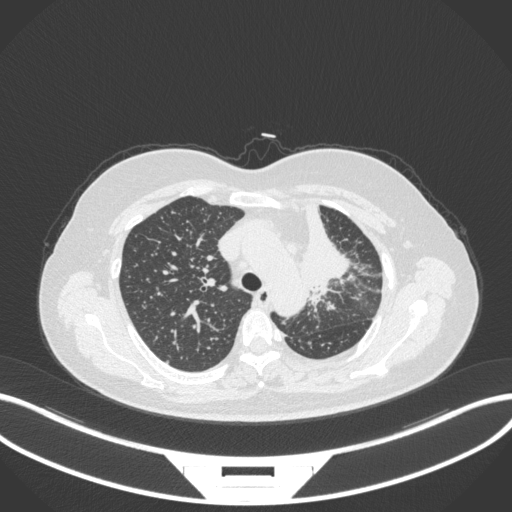
Chest CT, one axial slice; position 245 of 348 along the scan axis; reconstruction kernel B31f; 120 kVp; lung window (W 1500 / L -600 HU); 512 × 512 image matrix. Female patient, age 49 years. From the clinical record (not read from this slice): clinical TNM (as recorded): T1c N0 M1.
Structures marked on this image (rectangle marked by the reading radiologist):
- lung tumour (recorded histology: adenocarcinoma): bounding box <291,200,354,297> (left, top, right, bottom; pixels)